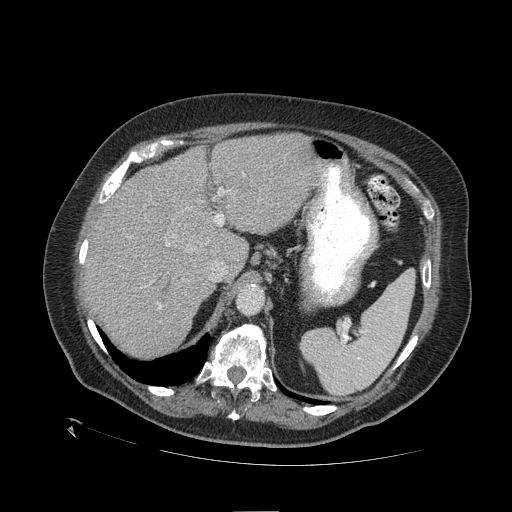
Contrast-enhanced abdominal CT (liver protocol), one axial slice; position 76 of 109 along the scan axis; reconstruction kernel STANDARD; one of 2 acquisitions stored at this slice position; soft-tissue window (W 400 / L 40 HU); 2.5 mm slice thickness; 512 × 512 image matrix. Case-level facts recorded for this patient, not image findings: diagnosis: hepatocellular carcinoma (patient treated with transarterial chemoembolisation; whether this scan precedes or follows treatment is not stated here); TNM stage (as recorded): Stage-I; Child-Pugh class: A; tumour differentiation: no biopsy; tumour nodularity: uninodular.
Annotated regions visible in this slice (semi-automatically segmented with operator editing):
- liver parenchyma outside the tumour (the mass and vessels are separate outlines, so this box may not span the whole liver): bounding box (x1, y1, x2, y2) in pixels: (84, 134, 316, 356)
- mass: (171, 208, 210, 252)
- liver vessels: (158, 187, 225, 309)